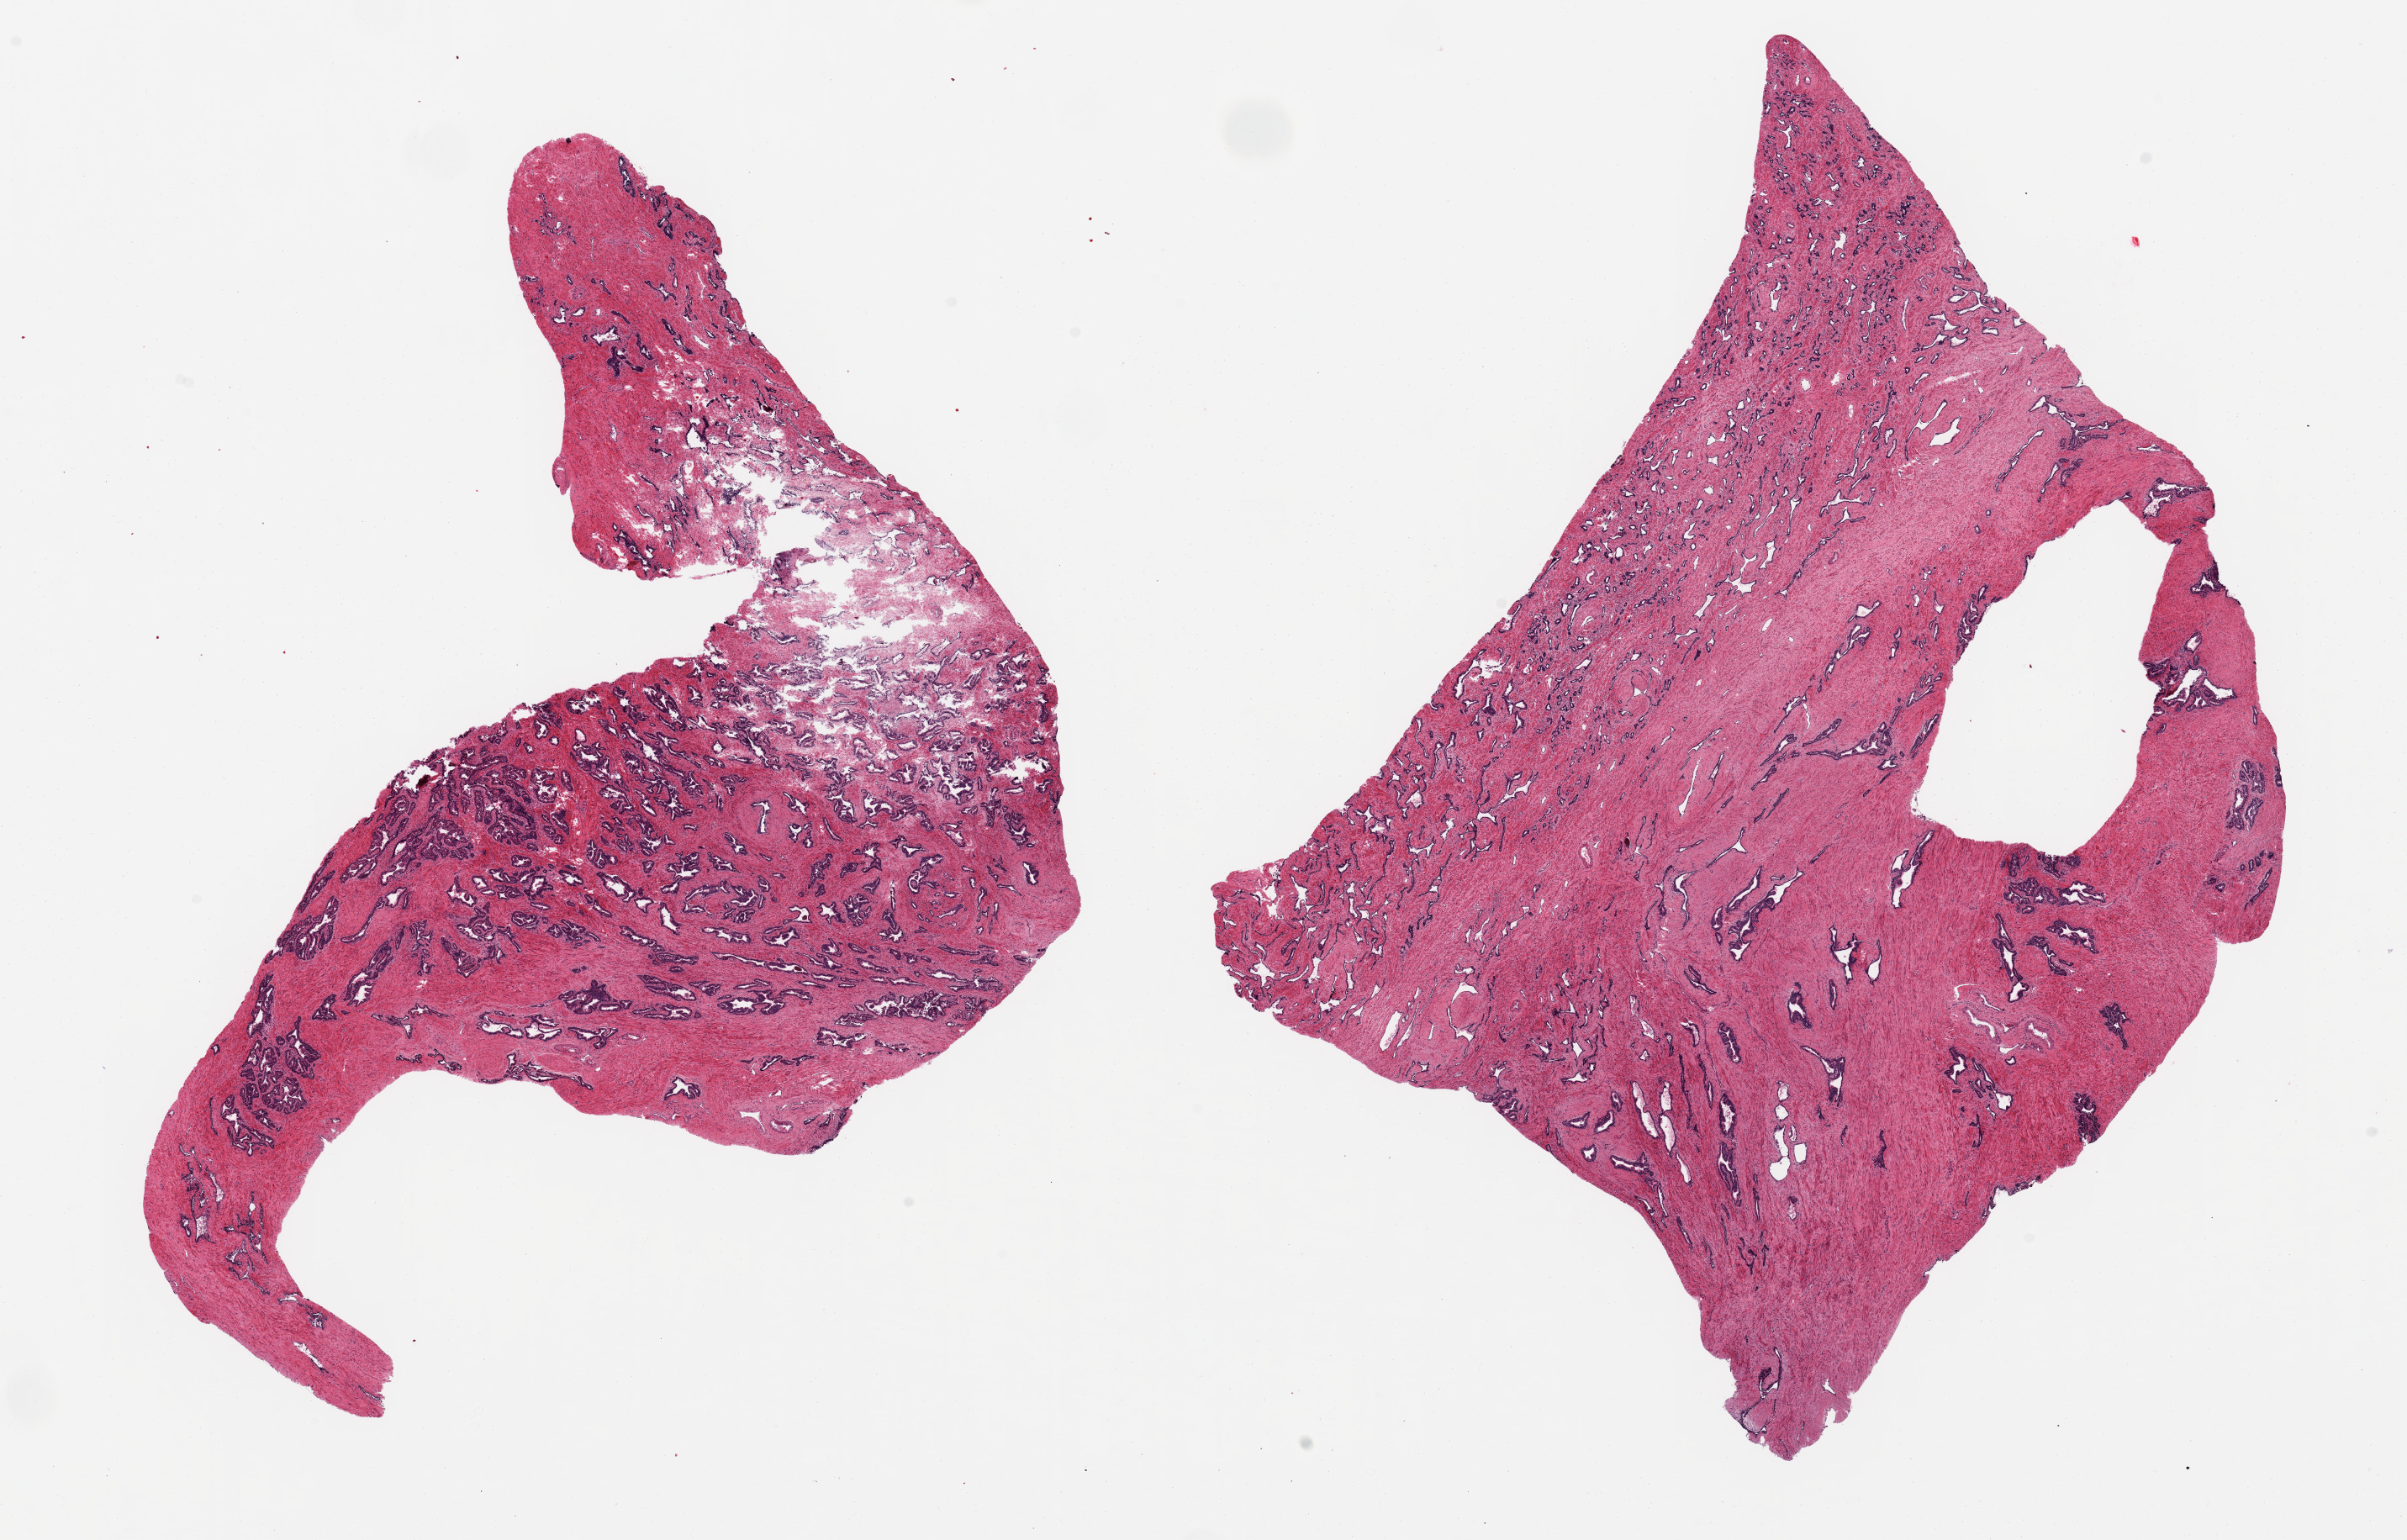
H&E whole-slide image, whole scanned area (about 22.6 x 14.5 mm) shown as a low-resolution overview, PAXgene-fixed paraffin-embedded (PFPE) section, section of prostate (target tissue), tissue donor sample. Donor: male.
Review note (as recorded): 2 ~9x6mm aliquots, patchy glandular hyperplasia.